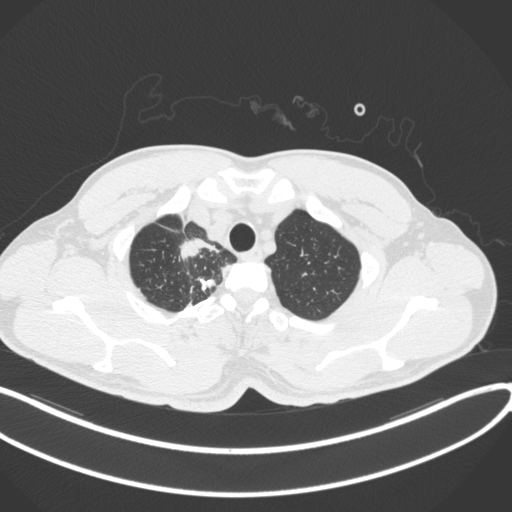
Chest CT, one axial slice. Position 332 of 391 along the scan axis. 120 kVp. Lung window (W 1500 / L -600 HU). 1 mm slice thickness. 512 × 512 image matrix, field of view 400 × 400 mm. Male patient, age 48 years. Case-level facts recorded for this patient, not image findings: clinical TNM (as recorded): T1c N1 M1.
Annotated regions visible in this slice (bounding box drawn by a radiologist):
- lung tumour (recorded histology: adenocarcinoma): bounding box [x1, y1, x2, y2] px = [177, 232, 223, 265]